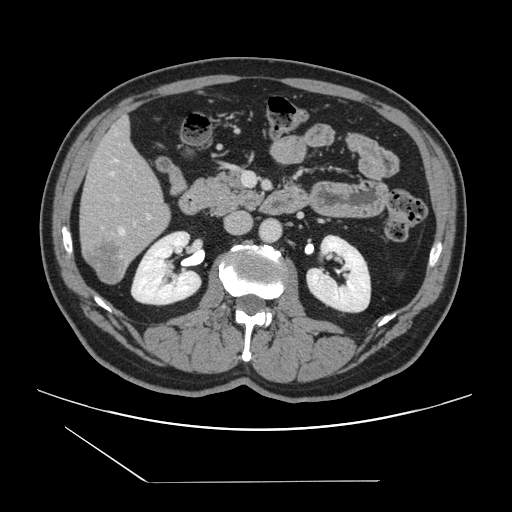
Contrast-enhanced abdominal CT, one axial slice; slice 55 of 157 in the series (ordered by position); 120 kVp; soft-tissue window (W 400 / L 40 HU); 2.5 mm slice thickness; 512 × 512 image matrix. Male patient, age 61 years. From the clinical record (not read from this slice): diagnosis: colorectal cancer liver metastases, imaged before liver resection; multiple liver metastases: yes; largest metastasis: 5.5 cm; disease in both lobes: yes.
Annotated regions visible in this slice (outlined manually by an expert reader):
- hepatic veins: bounding box (x1, y1, x2, y2) in pixels: (113, 159, 125, 235)
- liver: (81, 120, 171, 283)
- planned liver remnant (the part of the liver to remain after resection): (81, 121, 166, 218)
- portal vein (with intrahepatic branches): (117, 198, 151, 219)
- liver metastasis: (88, 242, 125, 283)